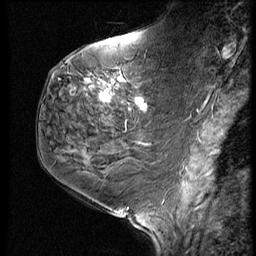
Breast MRI (dynamic contrast-enhanced), one sagittal slice. Slice 26 of 60 in the series (ordered by position). 3 images stored at this slice position (order not interpretable as contrast timing). 1.5 T. TE 4.2 ms, TR 9 ms. 2.5 mm slice thickness. 256 × 256 image matrix, field of view 180 × 180 mm. Patient: female, 59 years. From the clinical record (not read from this slice): setting: breast cancer imaged before/during neoadjuvant chemotherapy; receptor status: HER2-positive.
Annotated regions visible in this slice (semi-automatic segmentation, software-assisted and operator-edited):
- analysis volume of interest (the breast-tissue region the enhancement analysis was run in; not a lesion): bounding box [x1, y1, x2, y2] px = [78, 61, 161, 125]
- tumour enhancement mask (voxels above the 140 % enhancement threshold inside the analysis volume of interest): [86, 79, 146, 108]